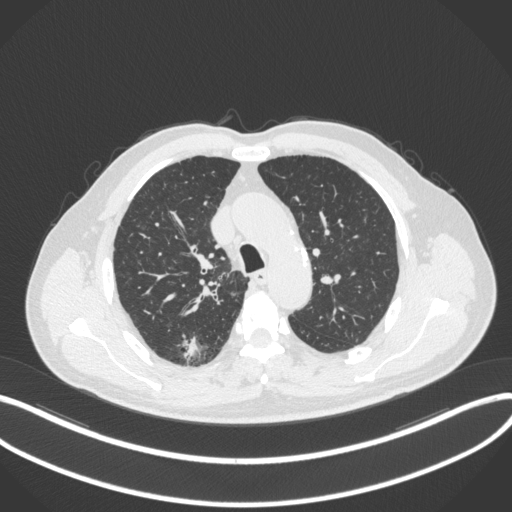
Chest CT, one axial slice; slice 270 of 366 in the series (ordered by position); reconstruction kernel B31f; lung window (W 1500 / L -600 HU); 1 mm slice thickness; 512 × 512 image matrix, field of view 400 × 400 mm. Patient: male, 69 years. Case-level facts recorded for this patient, not image findings: clinical TNM (as recorded): T1b N0 M0; histopathological grade: G2-3.
Outlined on this slice (rectangle marked by the reading radiologist):
- lung tumour (recorded histology: adenocarcinoma): bounding box (x1, y1, x2, y2) in pixels: (181, 333, 201, 362)